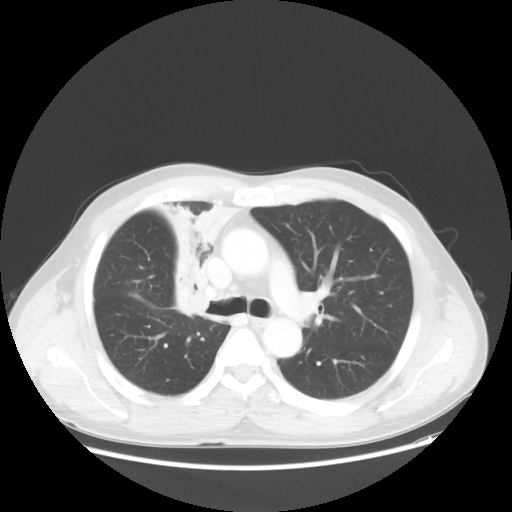
Chest CT, one axial slice; slice 35 of 56 in the series (ordered by position); reconstruction kernel STANDARD; 100 kVp; lung window (W 1500 / L -600 HU); 5 mm slice thickness; 512 × 512 image matrix. Patient: male, 60 years. From the clinical record (not read from this slice): clinical TNM (as recorded): T2a N1 M0.
Outlined on this slice (bounding box drawn by a radiologist):
- lung tumour (recorded histology: squamous cell carcinoma): bounding box (x1, y1, x2, y2) in pixels: (146, 189, 259, 336)